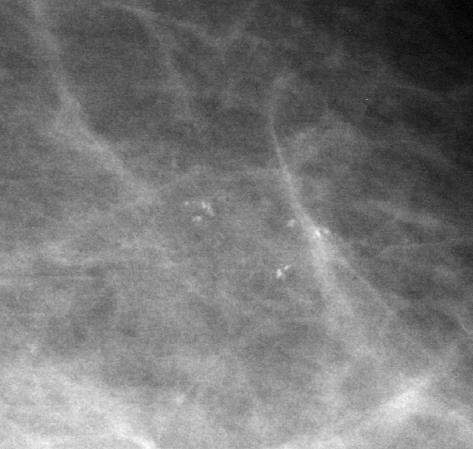
Region of interest cut from a scanned film mammogram (one marked finding); left breast; MLO view.
Finding: calcifications, morphology pleomorphic, distribution clustered; BI-RADS assessment category 4; subtlety rating 3 on a 1 (subtle) to 5 (obvious) scale; pathology result (as recorded, not read from the image): benign.